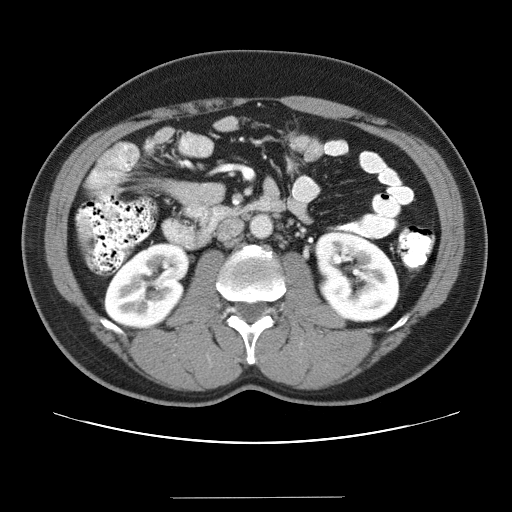
Contrast-enhanced abdominal CT (liver protocol), one axial slice. Slice 4 of 40 in the series (ordered by position). Reconstruction kernel STANDARD. Soft-tissue window (W 400 / L 40 HU). 512 × 512 image matrix, field of view 380 × 380 mm. From the clinical record (not read from this slice): diagnosis: hepatocellular carcinoma (patient treated with transarterial chemoembolisation; whether this scan precedes or follows treatment is not stated here); TNM stage (as recorded): Stage-IVA; Child-Pugh class: B.
Annotated regions visible in this slice (semi-automatically segmented with operator editing):
- liver parenchyma outside the tumour (the mass and vessels are separate outlines, so this box may not span the whole liver): bounding box [x1, y1, x2, y2] px = [76, 208, 91, 242]
- liver vessels: [77, 208, 92, 224]